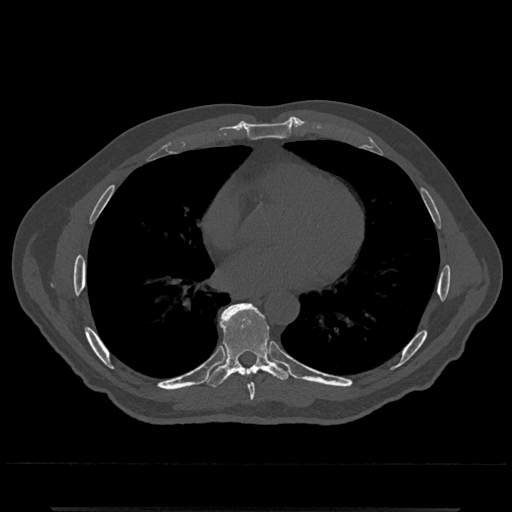
CT including the spine, one axial slice; position 684 of 797 along the scan axis; 120 kVp; bone window (W 1800 / L 400 HU); 0.5 mm slice thickness; 512 × 512 image matrix, field of view 393 × 393 mm. Male patient, age 67 years. From the clinical record (not read from this slice): primary cancer: prostate.
Structures marked on this image (semi-automatically segmented with operator editing):
- T7 vertebra: bounding box [x1, y1, x2, y2] px = [248, 384, 255, 404]
- T8 vertebra: [203, 303, 293, 388]